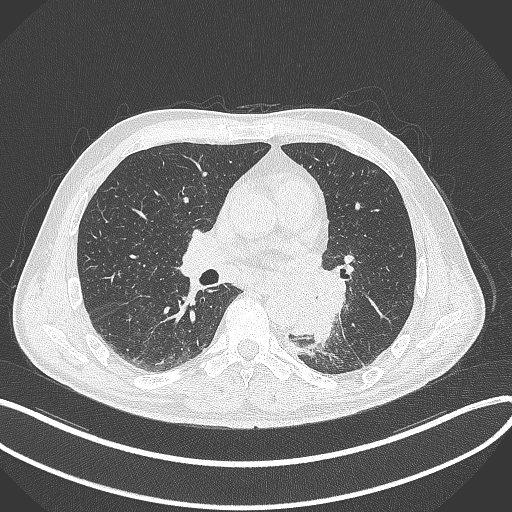
Chest CT, one axial slice. Slice 173 of 329 in the series (ordered by position). Reconstruction kernel B70f. 120 kVp. Lung window (W 1500 / L -600 HU). 512 × 512 image matrix, field of view 400 × 400 mm. Male patient, age 59 years. Case-level facts recorded for this patient, not image findings: clinical TNM (as recorded): T2a N2 M0.
Outlined on this slice (bounding box drawn by a radiologist):
- lung tumour (recorded histology: squamous cell carcinoma): bounding box (x1, y1, x2, y2) in pixels: (273, 256, 346, 342)